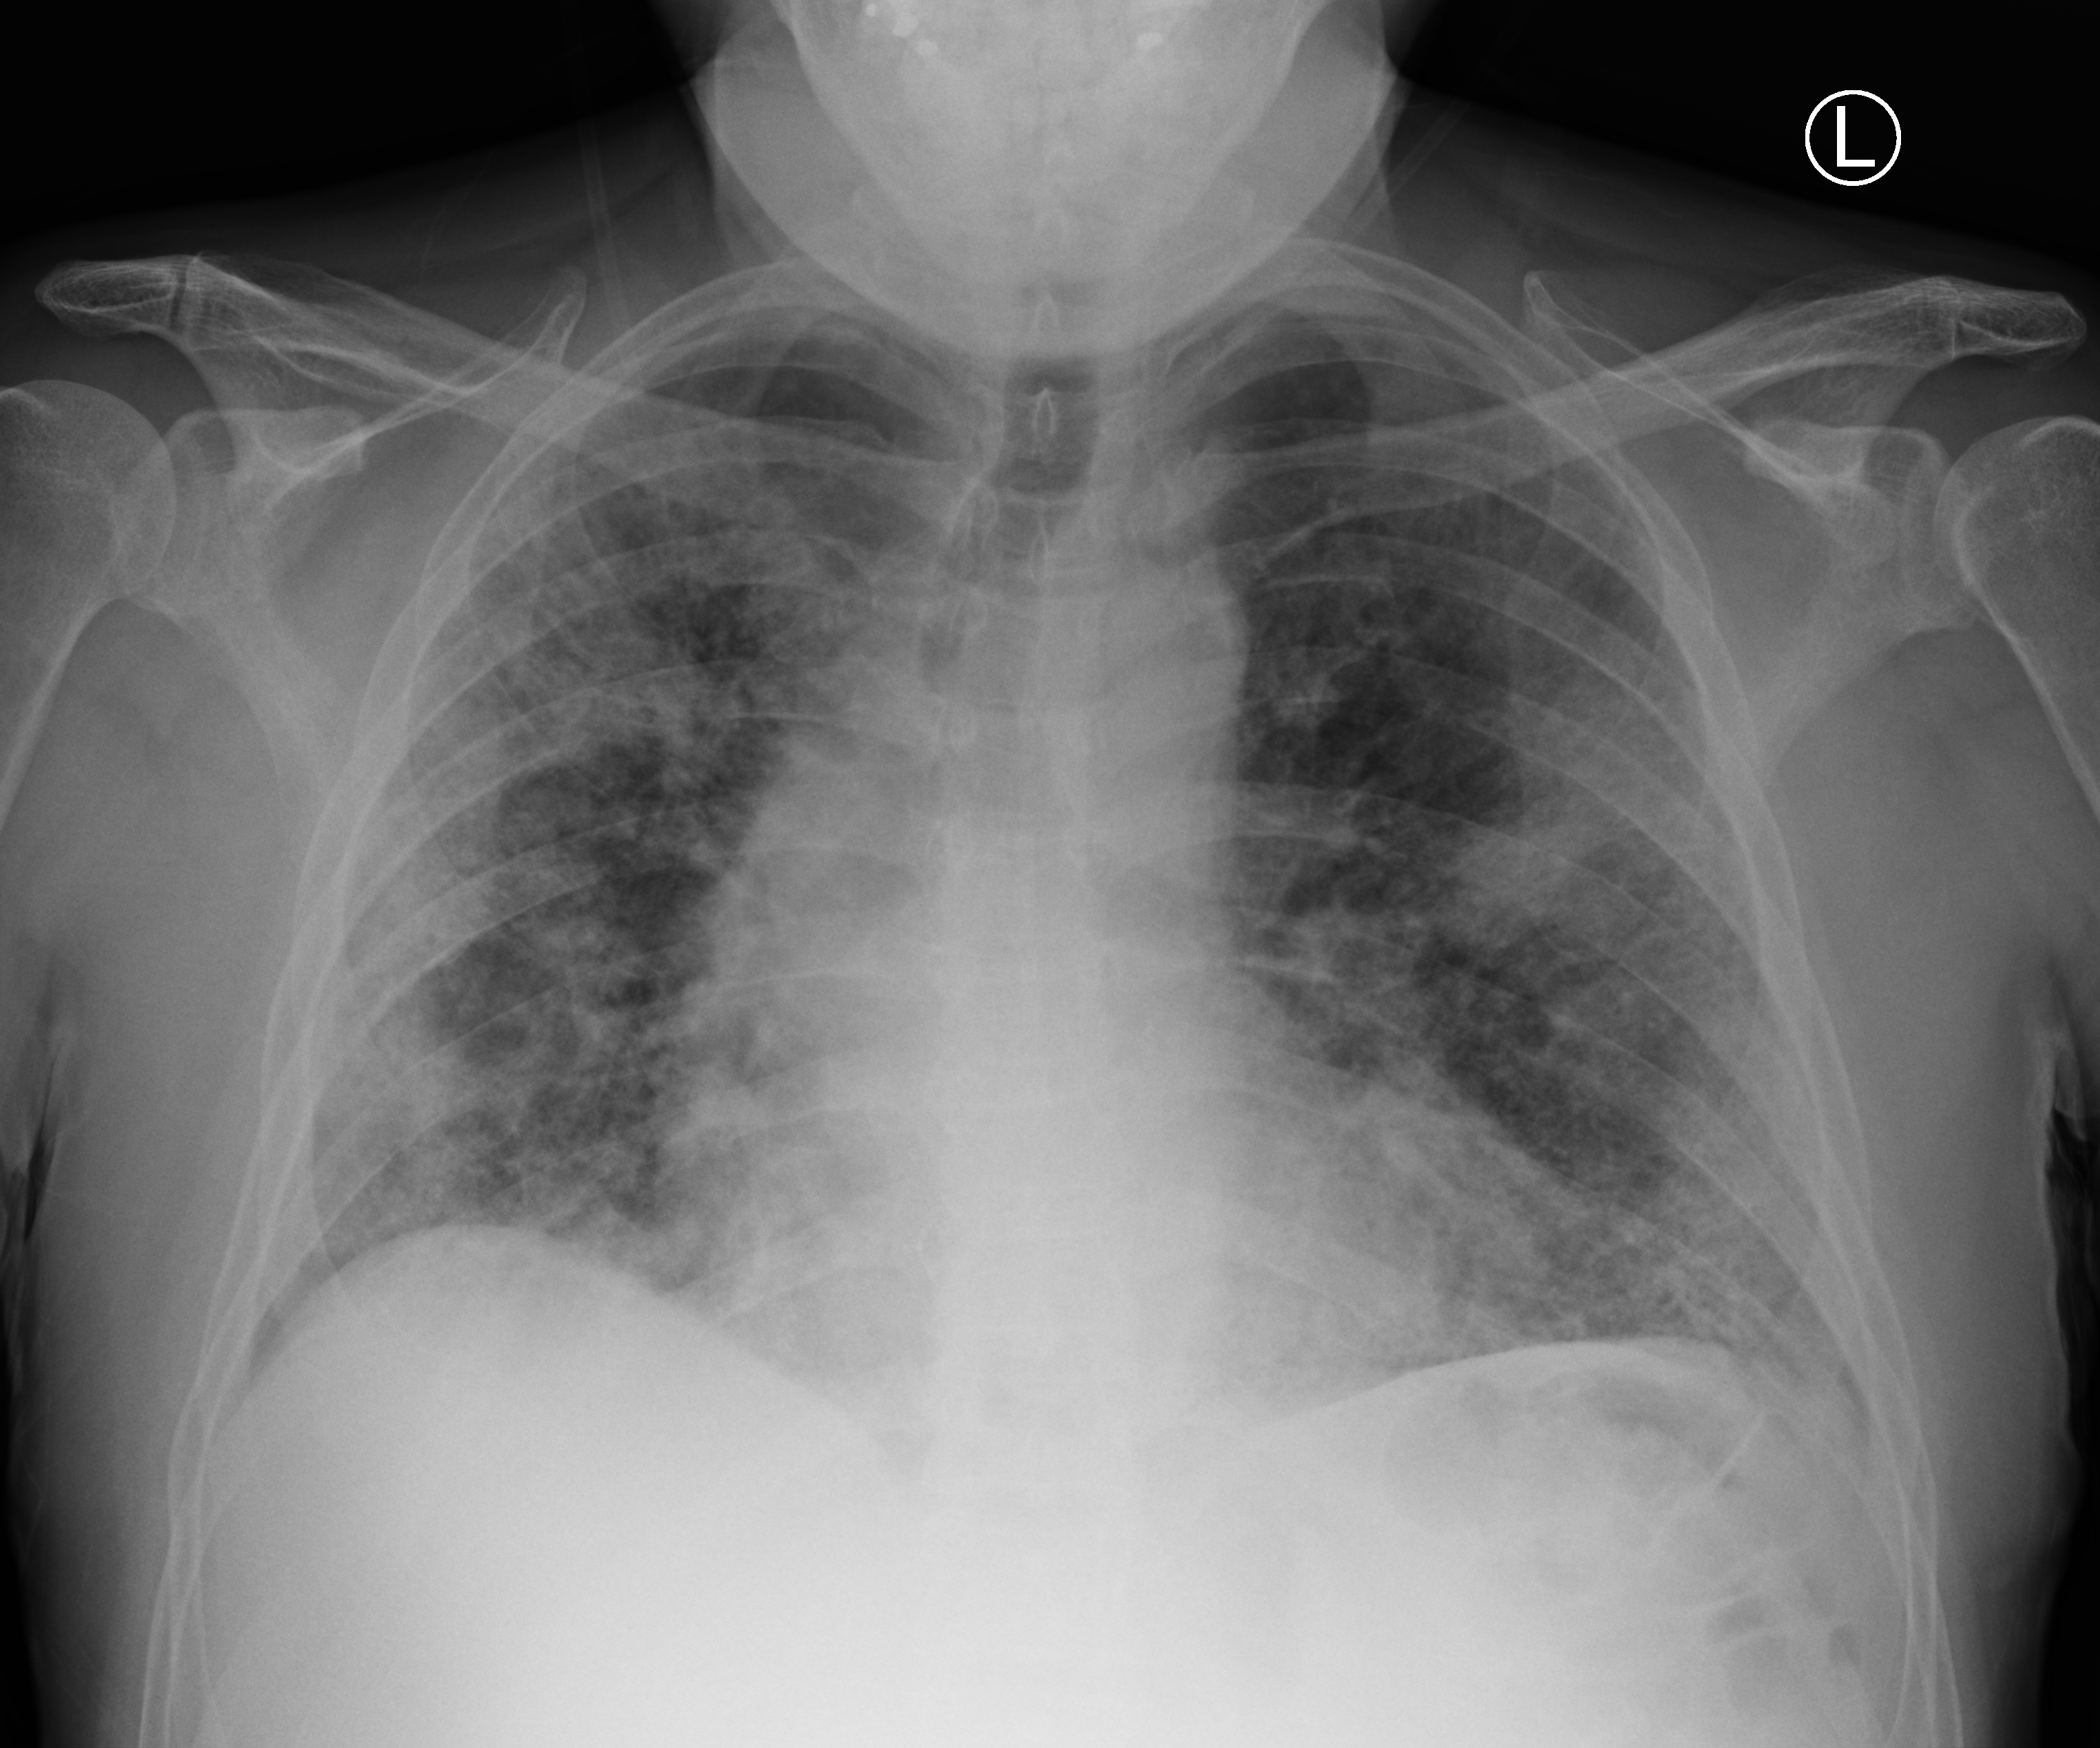
Chest X-ray (portable). Male patient hospitalised with COVID-19, age 60–74 years.
Hospital-stay facts (about this admission, not read from this image; timing relative to this image not recorded): admitted to intensive care during this hospital stay: yes.